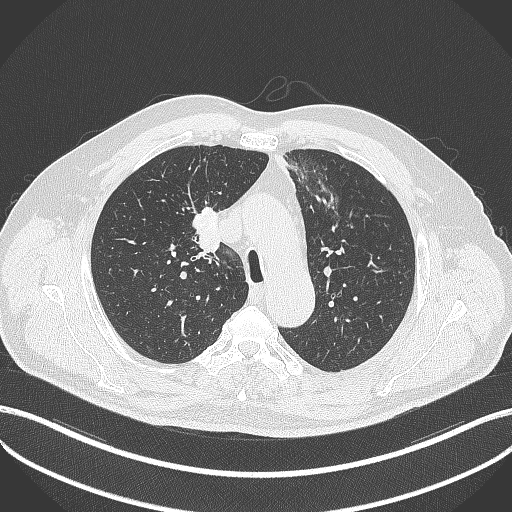
Chest CT, one axial slice. Slice 281 of 411 in the series (ordered by position). 120 kVp. Lung window (W 1500 / L -600 HU). 512 × 512 image matrix, field of view 400 × 400 mm. Male patient, age 60 years. From the clinical record (not read from this slice): clinical TNM (as recorded): T1b N1 M0.
Outlined on this slice (bounding box drawn by a radiologist):
- lung tumour (recorded histology: squamous cell carcinoma): bounding box <192,207,222,255> (left, top, right, bottom; pixels)